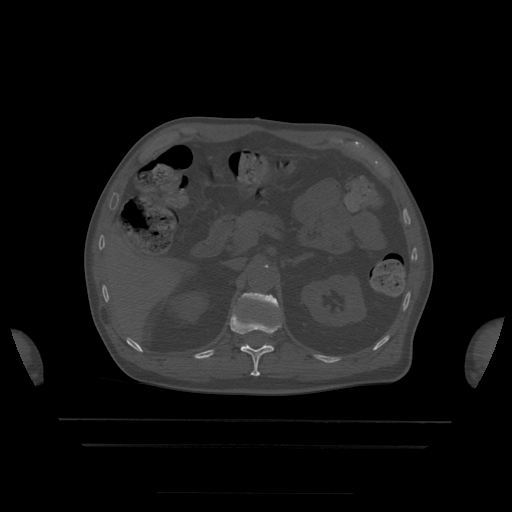
CT including the spine, one axial slice. Slice 188 of 522 in the series (ordered by position). Bone window (W 1800 / L 400 HU). 1.25 mm slice thickness. 512 × 512 image matrix, field of view 436 × 436 mm. Patient age 68 years. Case-level facts recorded for this patient, not image findings: primary cancer: urothelial.
Structures marked on this image (semi-automatically segmented with operator editing):
- L1 vertebra: bounding box <241,293,279,310> (left, top, right, bottom; pixels)
- T12 vertebra: <230,309,281,377>